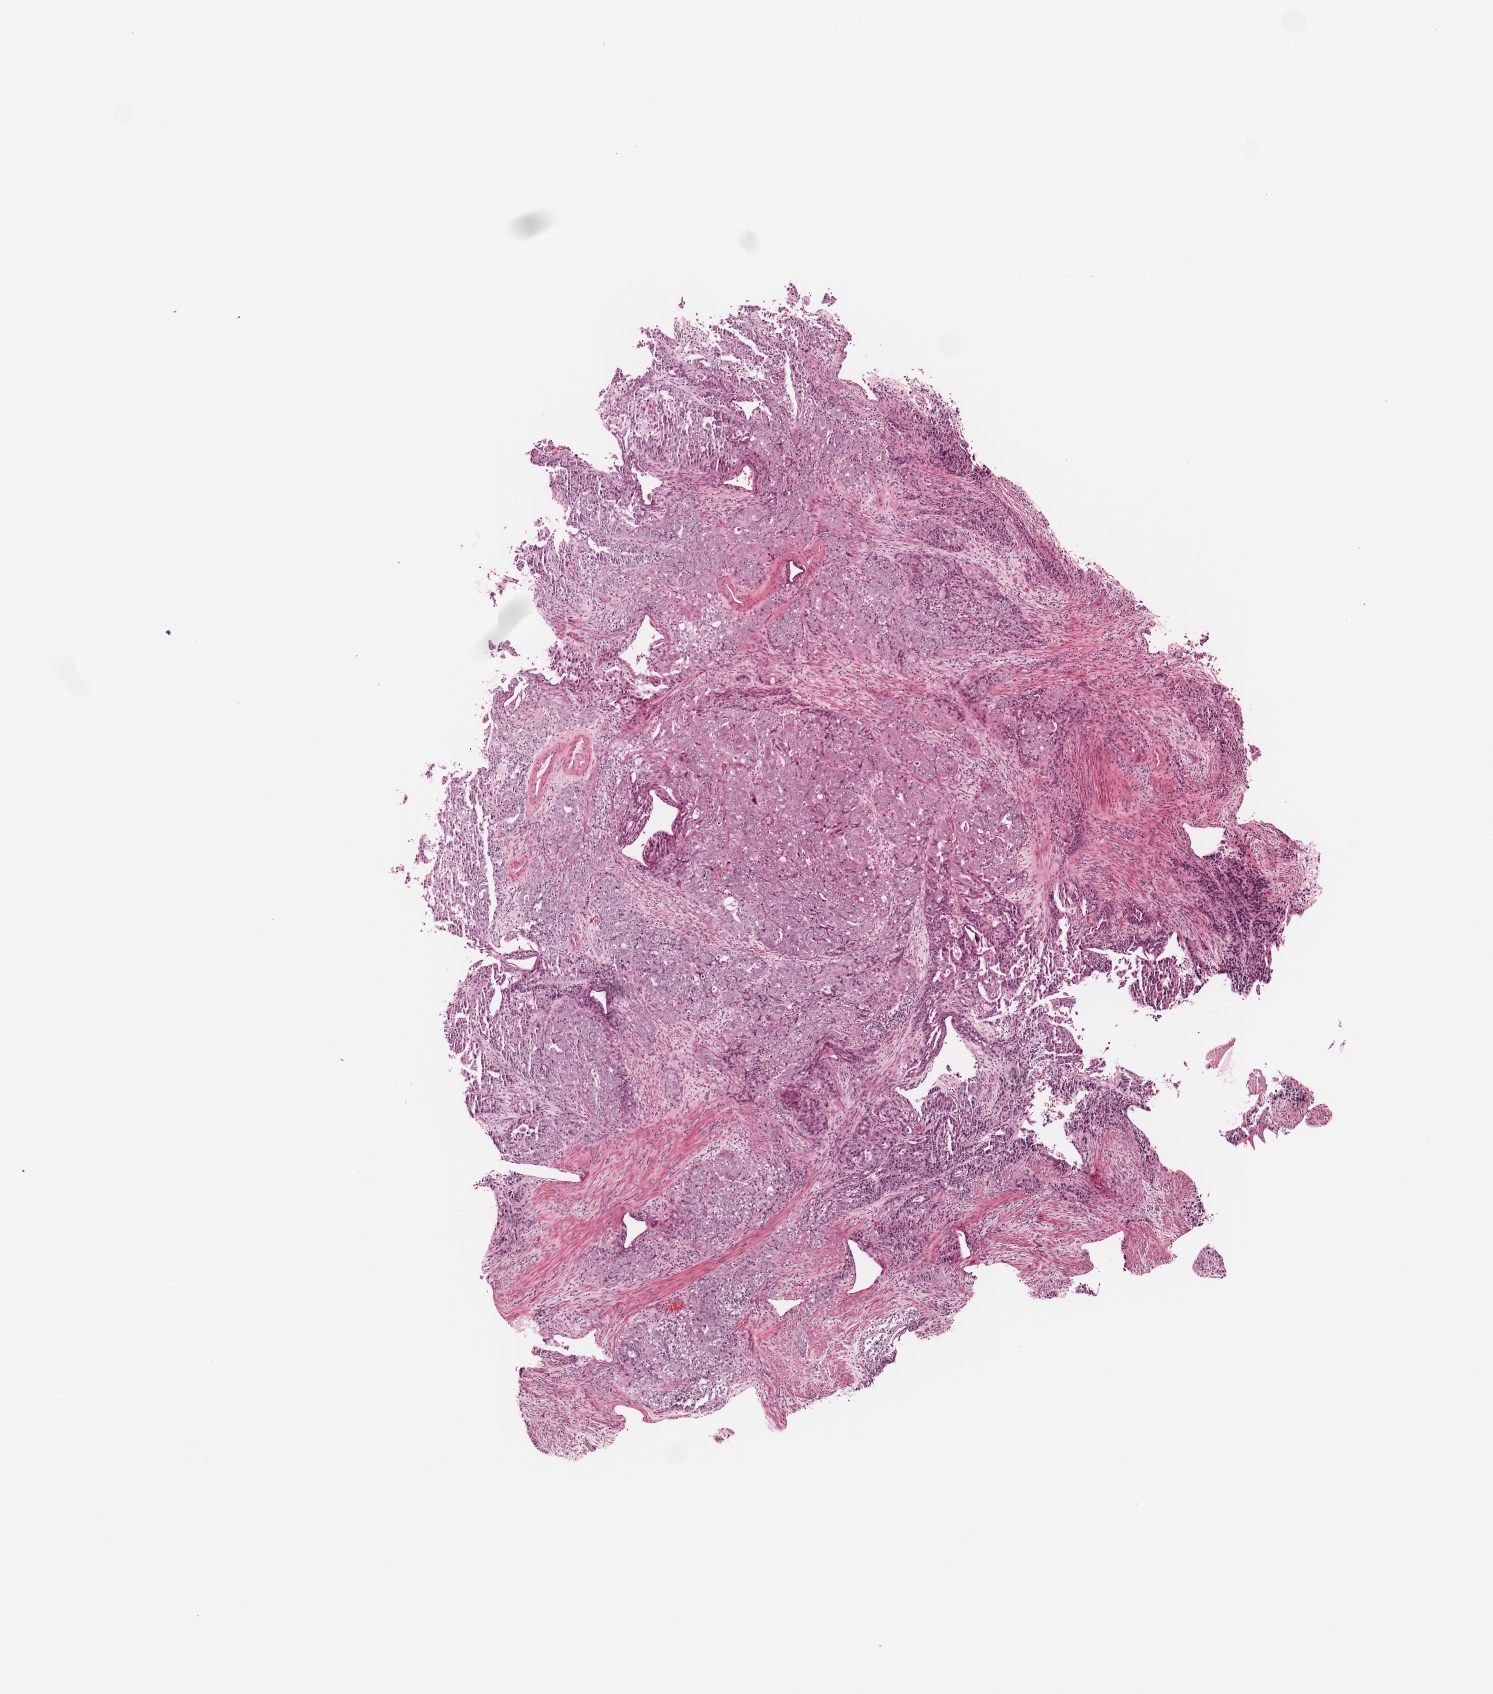
Hematoxylin and eosin (H&E) stained whole-slide image — low-resolution overview of the scanned area, about 5.9 x 6.7 mm, tumour tissue sample, sampled site: uterus. 59-year-old female patient. Histologic grade: G3 (poorly differentiated). Slide review estimates, as recorded: tumour nuclei 85%, necrosis 2%.
- diagnosis: Endometrioid adenocarcinoma, NOS
- AJCC pathologic stage: I